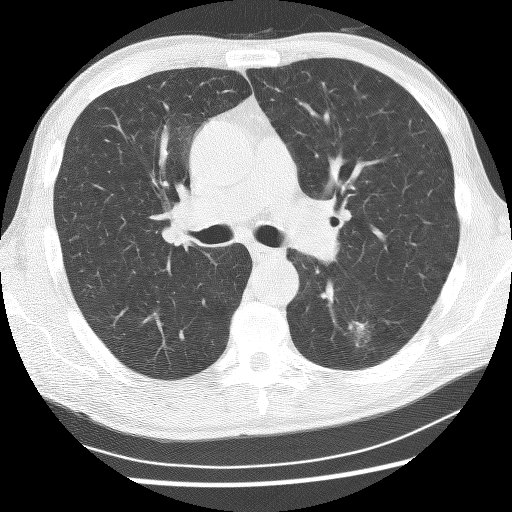
Axial slice from a low-dose chest CT screening exam. Baseline screening round. Lung window (W 1500 / L -600 HU). 2.5 mm slice thickness. Lung (sharp) reconstruction kernel (BONE). Slice 101 of 253 in the series. 512 × 512 image matrix. Male participant, aged 62 years at enrolment. Current smoker at enrolment.
Lesion marked by an expert reader, bounding box <332,309,380,356> (left, top, right, bottom; pixels). Screening reader's record for this exam (one nodule recorded; not confirmed to be the boxed lesion): non-calcified nodule or mass ≥4 mm, left lower lobe, 21 × 17 mm, spiculated (stellate) margins, soft tissue attenuation. Official screen result: positive, change unspecified: nodule(s) >= 4 mm or enlarging nodule(s), mass(es), or other non-specific abnormalities suspicious for lung cancer. Lung cancer was diagnosed 58 days after this screen: non-small cell carcinoma, left lower lobe, poorly differentiated (G3), stage IA (AJCC 6th edition), 11 mm at pathology.